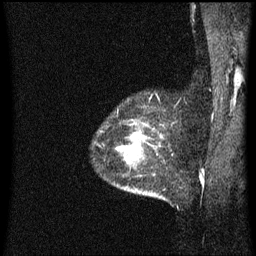
Breast MRI (dynamic contrast-enhanced), one sagittal slice; position 52 of 60 along the scan axis; dynamic contrast-enhanced series, image 2 of 3 at this slice position (ordered by acquisition); 1.5 T; TE 4.2 ms, TR 8.4 ms; 256 × 256 image matrix. Patient: female, 34 years. Case-level facts recorded for this patient, not image findings: setting: breast cancer imaged before/during neoadjuvant chemotherapy; receptor status: HR-positive, HER2-negative.
Annotated regions visible in this slice (semi-automatically segmented with operator editing):
- analysis volume of interest (the breast-tissue region the enhancement analysis was run in; not a lesion): bounding box <117,134,167,201> (left, top, right, bottom; pixels)
- tumour enhancement mask (voxels above the 70 % enhancement threshold inside the analysis volume of interest): <136,136,145,149>